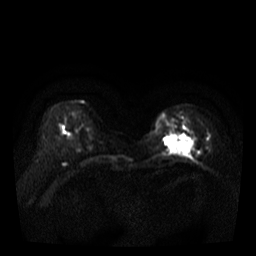
Breast MRI, one axial slice; diffusion-weighted series; image 2 of 4 stored at this slice position (different b-values; order by instance number); 3 T; 5 mm slice thickness; 256 × 256 image matrix. Female patient.
Outlined on this slice (outlined manually by an expert reader):
- tumour on diffusion-weighted imaging: bounding box <163,134,193,153> (left, top, right, bottom; pixels)